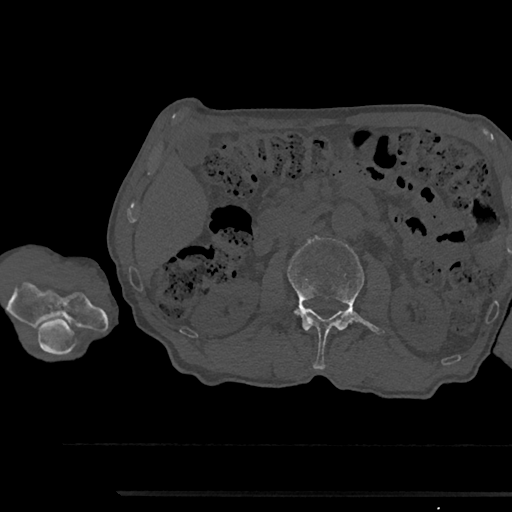
CT including the spine, one axial slice; position 562 of 797 along the scan axis; reconstruction kernel Br40s/3; bone window (W 1800 / L 400 HU); 512 × 512 image matrix, field of view 367 × 367 mm. Male patient, age 79 years. From the clinical record (not read from this slice): primary cancer: prostate.
Structures marked on this image (semi-automatically segmented with operator editing):
- L2 vertebra: box from (x=287, y=236) to (x=382, y=369) px